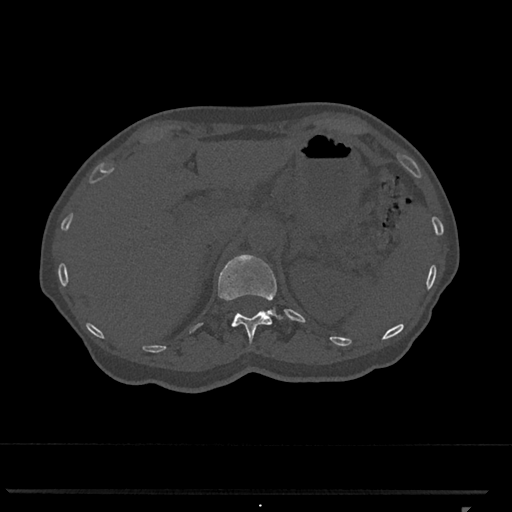
CT including the spine, one axial slice; reconstruction kernel Br40s/3; 120 kVp; bone window (W 1800 / L 400 HU); 512 × 512 image matrix, field of view 380 × 380 mm. Female patient, age 62 years. From the clinical record (not read from this slice): primary cancer: renal.
Annotated regions visible in this slice (semi-automatic segmentation, software-assisted and operator-edited):
- T12 vertebra: bounding box [x1, y1, x2, y2] px = [218, 255, 283, 345]